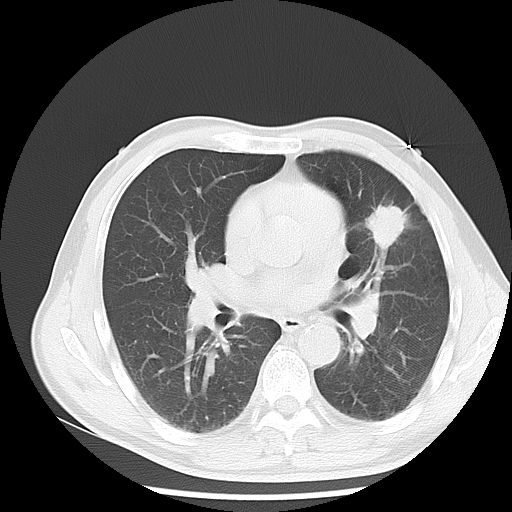
Chest CT, one axial slice. Slice 8 of 13 in the series (ordered by position). Reconstruction kernel LUNG. 120 kVp. Lung window (W 1500 / L -600 HU). 512 × 512 image matrix. Patient: male, 54 years. Case-level facts recorded for this patient, not image findings: clinical TNM (as recorded): T1c N0 M0.
Structures marked on this image (rectangle marked by the reading radiologist):
- lung tumour (recorded histology: adenocarcinoma): bounding box (x1, y1, x2, y2) in pixels: (367, 200, 407, 253)